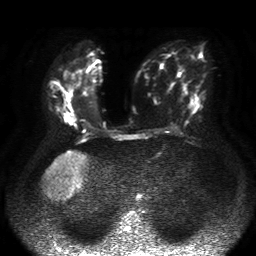
Breast MRI, one axial slice. Slice 23 of 50 in the series (ordered by position). Diffusion-weighted series; image 2 of 4 stored at this slice position (different b-values; order by instance number). 1.5 T. 4 mm slice thickness. 256 × 256 image matrix, field of view 360 × 360 mm. Female patient.
Structures marked on this image (outlined manually by an expert reader):
- tumour on diffusion-weighted imaging: bounding box [x1, y1, x2, y2] px = [64, 116, 72, 125]